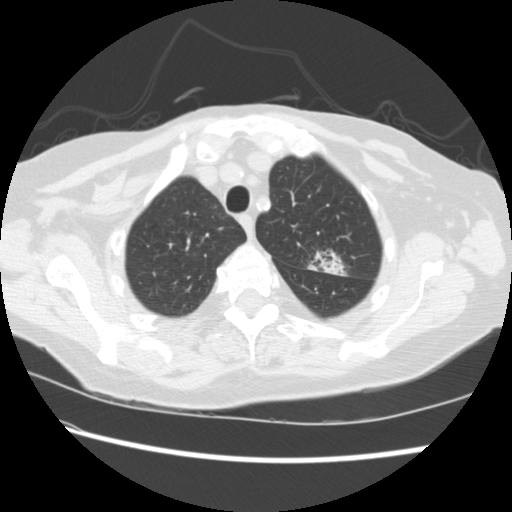
Low-dose screening chest CT, one axial slice. Position 180 of 224 along the scan axis. Reconstruction kernel STANDARD. 120 kVp. Lung window (W 1500 / L -600 HU). 2.5 mm slice thickness. 512 × 512 image matrix, field of view 340 × 340 mm.
Outlined on this slice (outlined manually by an expert reader):
- lesion 1 (tumor, upper lobe of left lung): bounding box (x1, y1, x2, y2) in pixels: (318, 257, 345, 276)